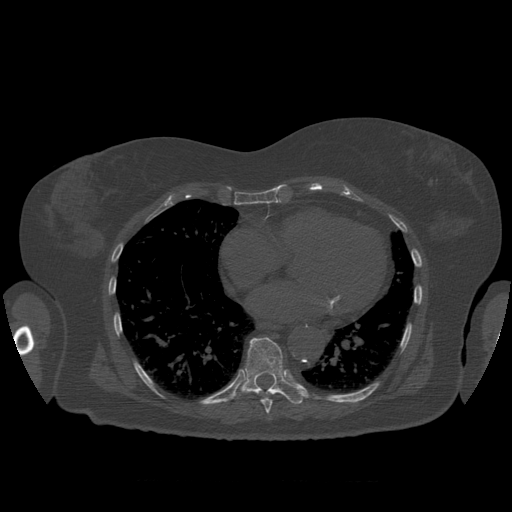
CT including the spine, one axial slice. Slice 366 of 399 in the series (ordered by position). Reconstruction kernel STANDARD. Bone window (W 1800 / L 400 HU). 1.25 mm slice thickness. 512 × 512 image matrix, field of view 404 × 404 mm. Patient age 81 years. Case-level facts recorded for this patient, not image findings: primary cancer: renal.
Outlined on this slice (semi-automatic segmentation, software-assisted and operator-edited):
- T8 vertebra: bounding box [x1, y1, x2, y2] px = [261, 395, 273, 414]
- T9 vertebra: [234, 338, 303, 405]